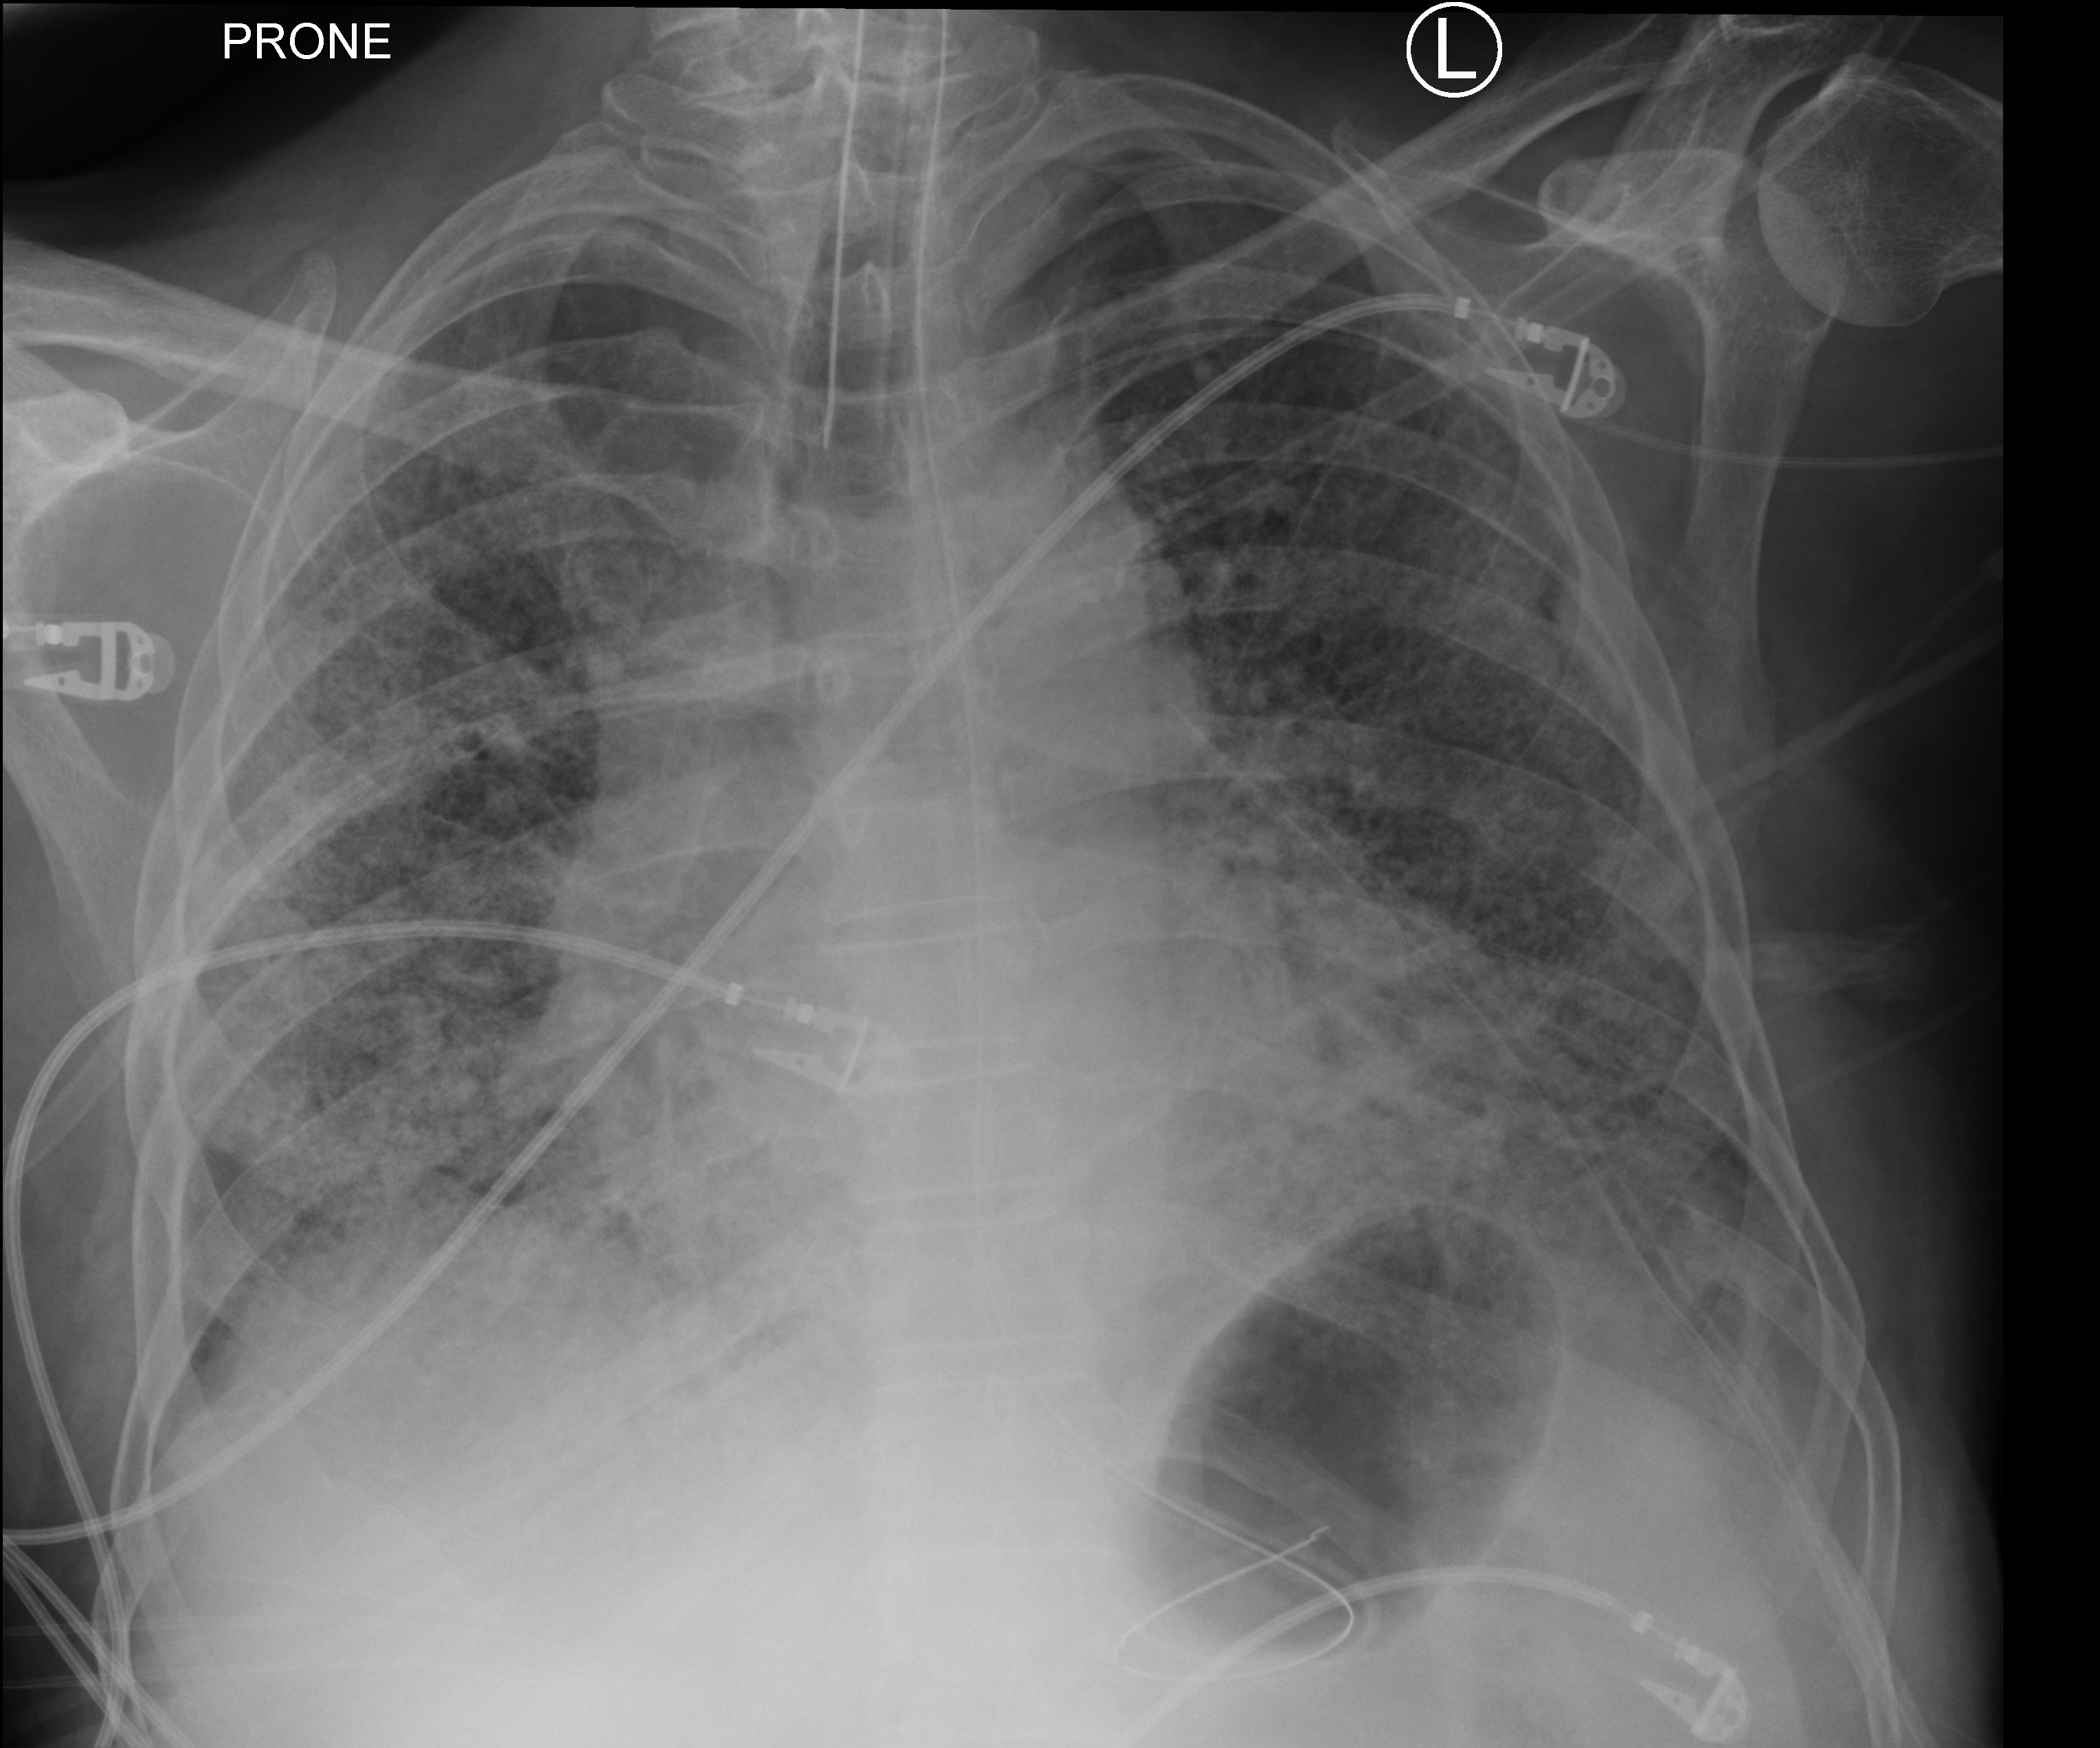
Chest X-ray (portable). Patient hospitalised with COVID-19; male, aged 60–74 years.
From the hospital-stay record, not from the radiograph (when in the stay this image was taken is not recorded):
- admitted to intensive care during this hospital stay: yes